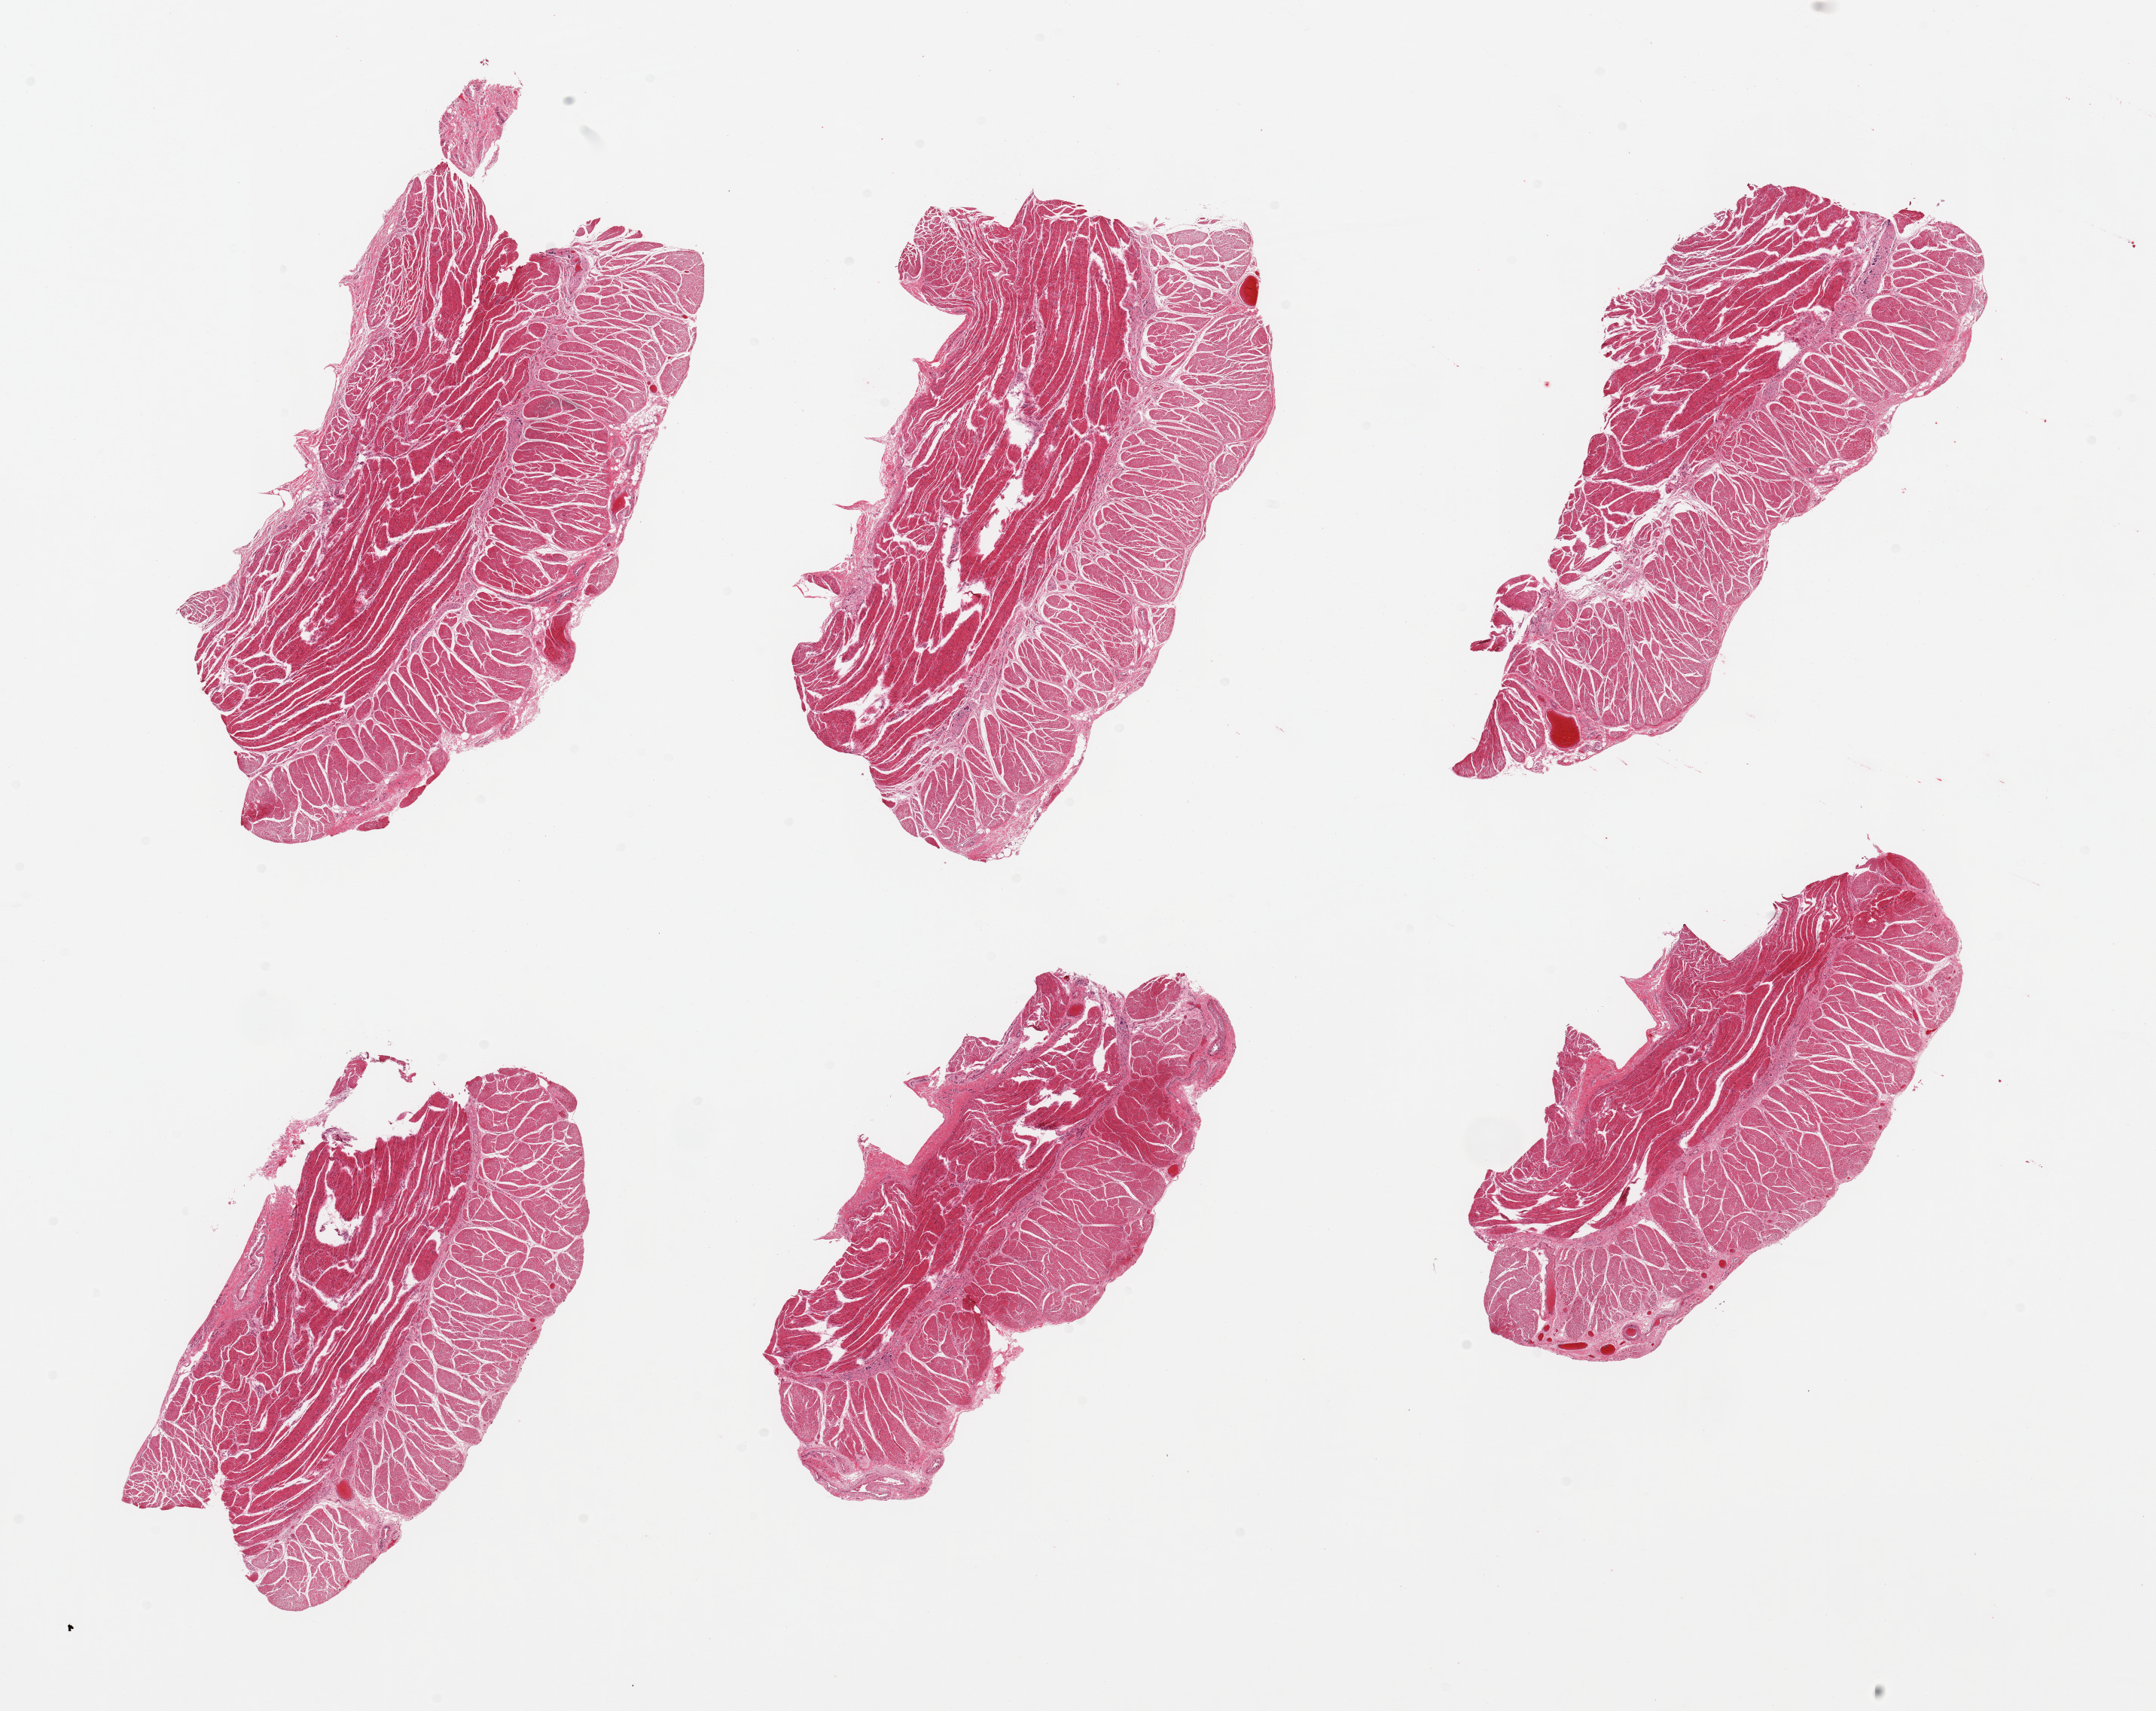
Digitized H&E-stained section, brightfield, shown as a low-resolution overview of the whole scanned area (about 22.6 x 18.0 mm, acquisition: 20x scan), PAXgene-fixed paraffin-embedded (PFPE) section, target tissue: gastroesophageal junction, tissue donor sample. Male donor.
Pathologist's review note for this sample: 6 pieces, confirmed target muscularis.